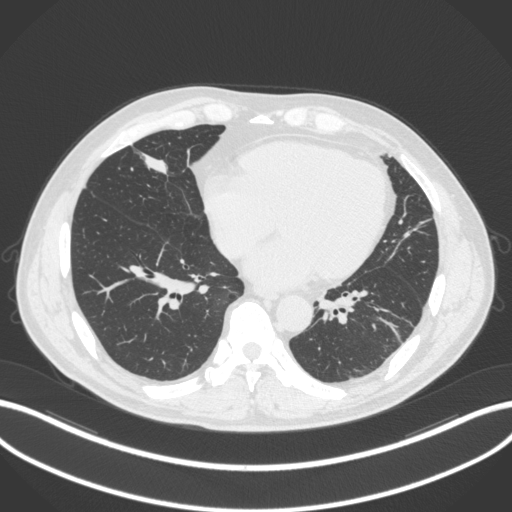
Chest CT, one axial slice. Position 96 of 399 along the scan axis. Reconstruction kernel B31f. 120 kVp. Lung window (W 1500 / L -600 HU). 512 × 512 image matrix. Patient: male, 59 years. From the clinical record (not read from this slice): clinical TNM (as recorded): T2a N1 M0.
Outlined on this slice (rectangle marked by the reading radiologist):
- lung tumour (recorded histology: adenocarcinoma): bounding box <130,144,173,184> (left, top, right, bottom; pixels)